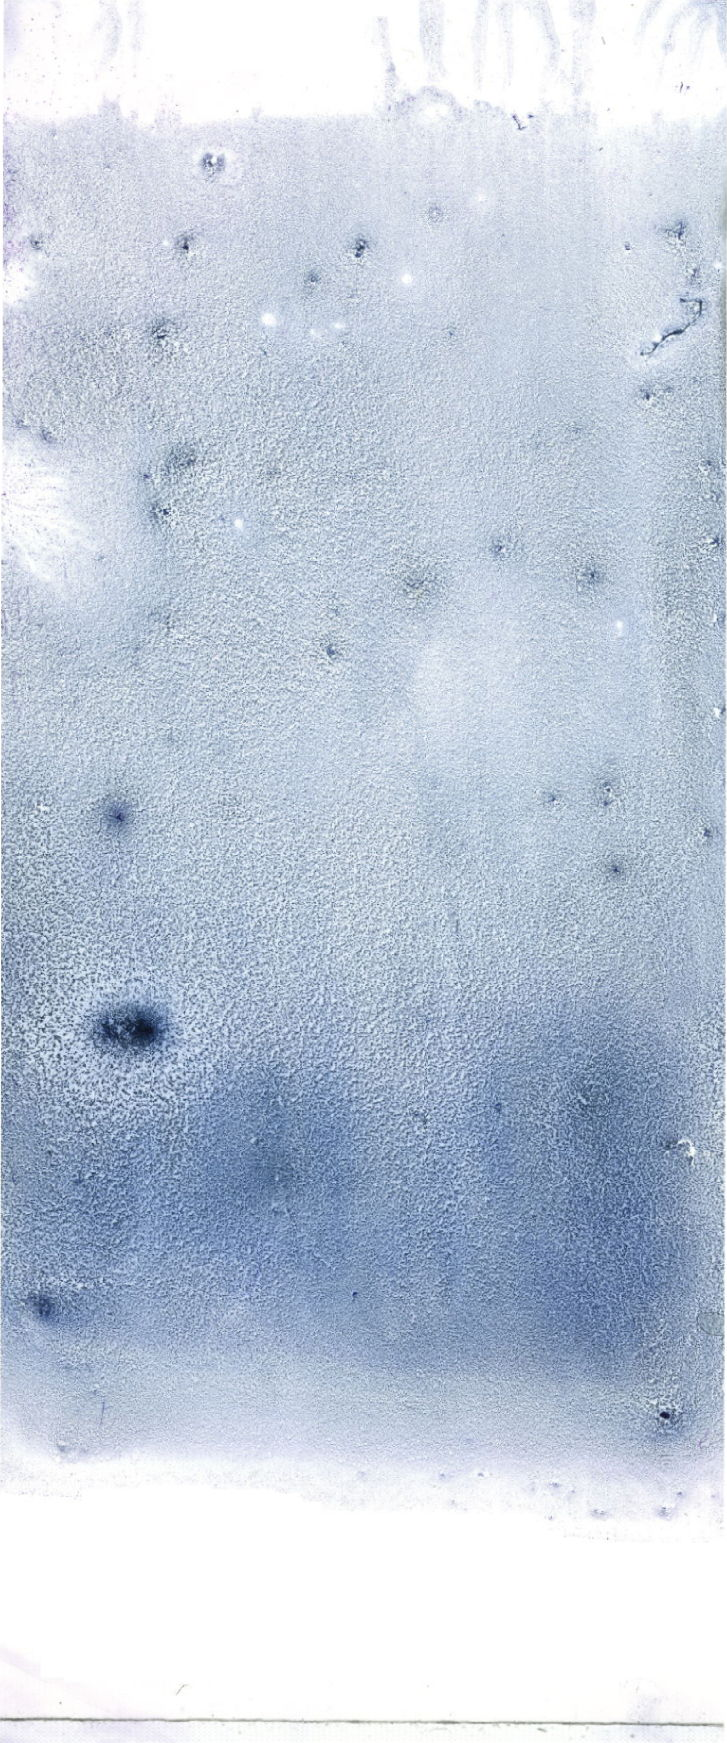
Bone marrow aspirate smear, May-Grünwald-Giemsa (MGG) stain, whole-slide image — a low-resolution overview of the entire scanned area, about 20.6 x 49.4 mm. Patient sex: female.
* diagnosis: Mixed Phenotype Acute Leukemia, B/Myeloid